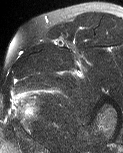
MRI of an extremity soft-tissue mass, one axial slice; slice 46 of 60 in the series (ordered by position); T2-weighted fat-saturated; MR volume resampled by the dataset authors to the PET/CT grid (not the native acquisition matrix); 3.27 mm slice thickness; 123 × 153 image matrix. Male patient. From the clinical record (not read from this slice): histological type: pleiomorphic liposarcoma; grade: high; site of the primary tumour: left thigh.
Structures marked on this image (expert contour drawn on MRI and transferred to this co-registered scan by the dataset authors):
- gross tumour volume including surrounding oedema: bounding box [x1, y1, x2, y2] px = [11, 97, 39, 119]